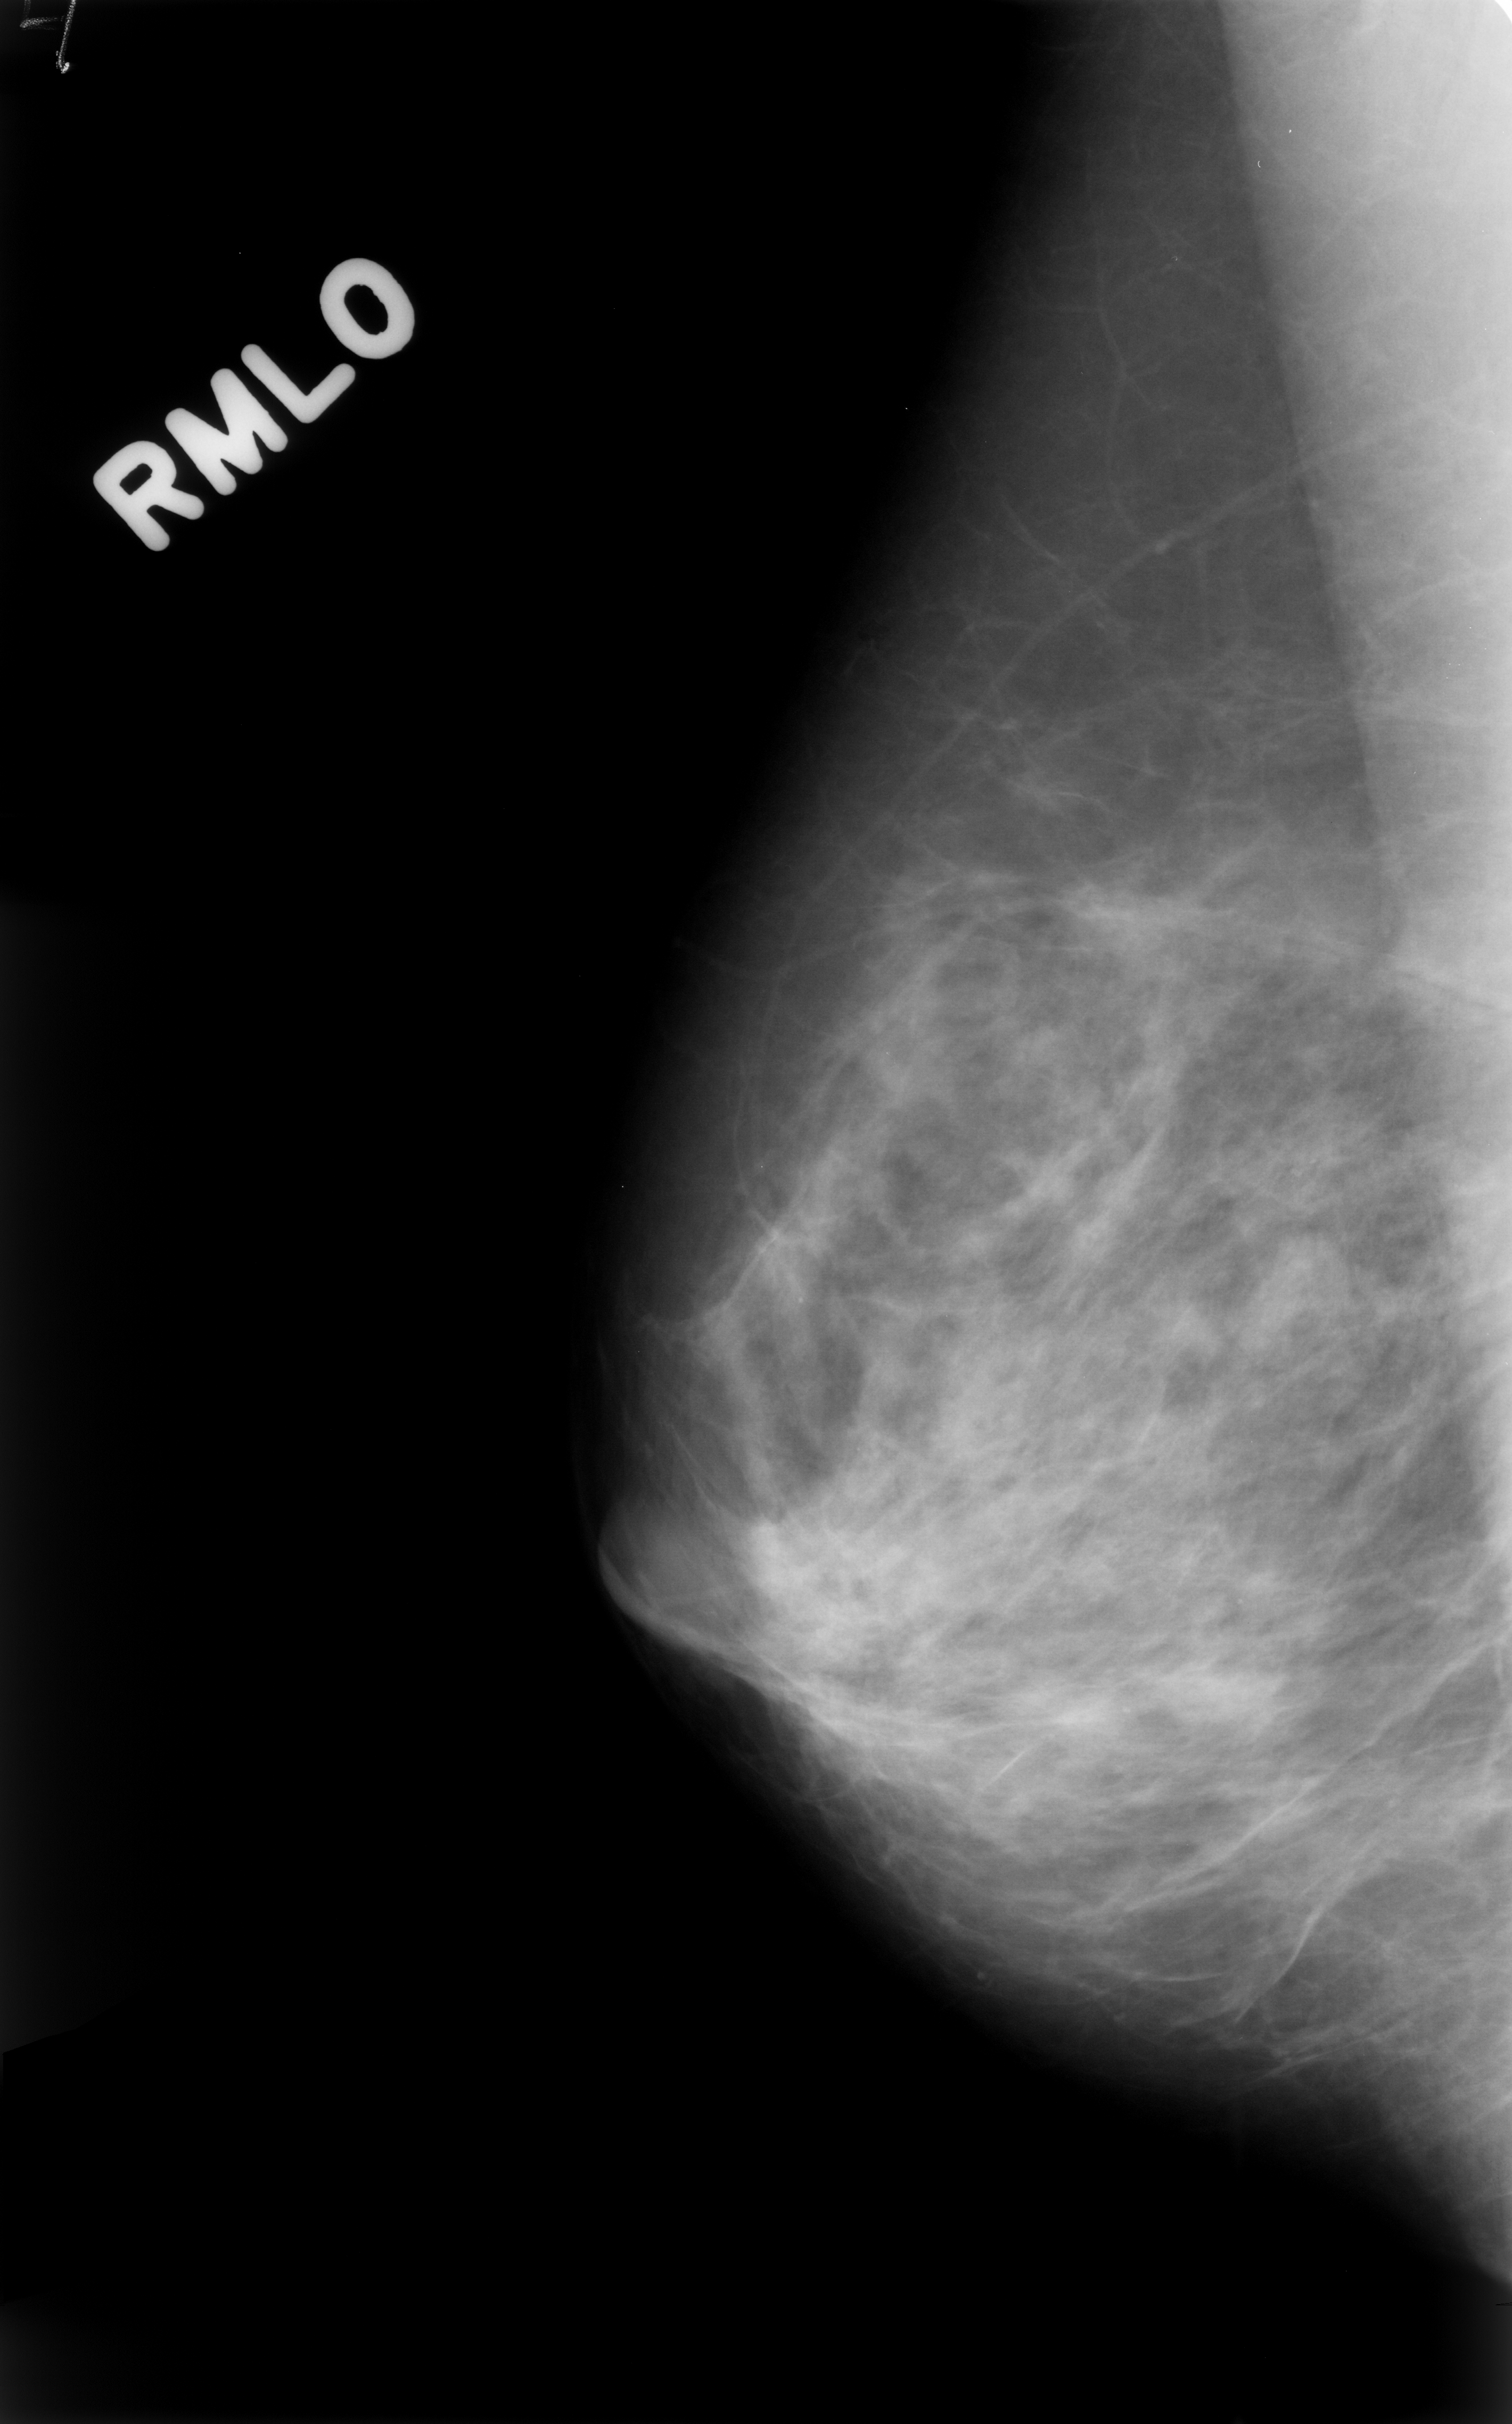
Mammogram (digitized film); right breast; MLO view; breast composition: scattered fibroglandular densities (BI-RADS density category 2 of 4); 1512 × 2424 image matrix.
Expert-marked regions of interest on this image (one box per marked abnormality):
- mass, shape lobulated, margins circumscribed; BI-RADS assessment category 4; pathology (as recorded): benign: box from (x=1225, y=1229) to (x=1389, y=1383) px